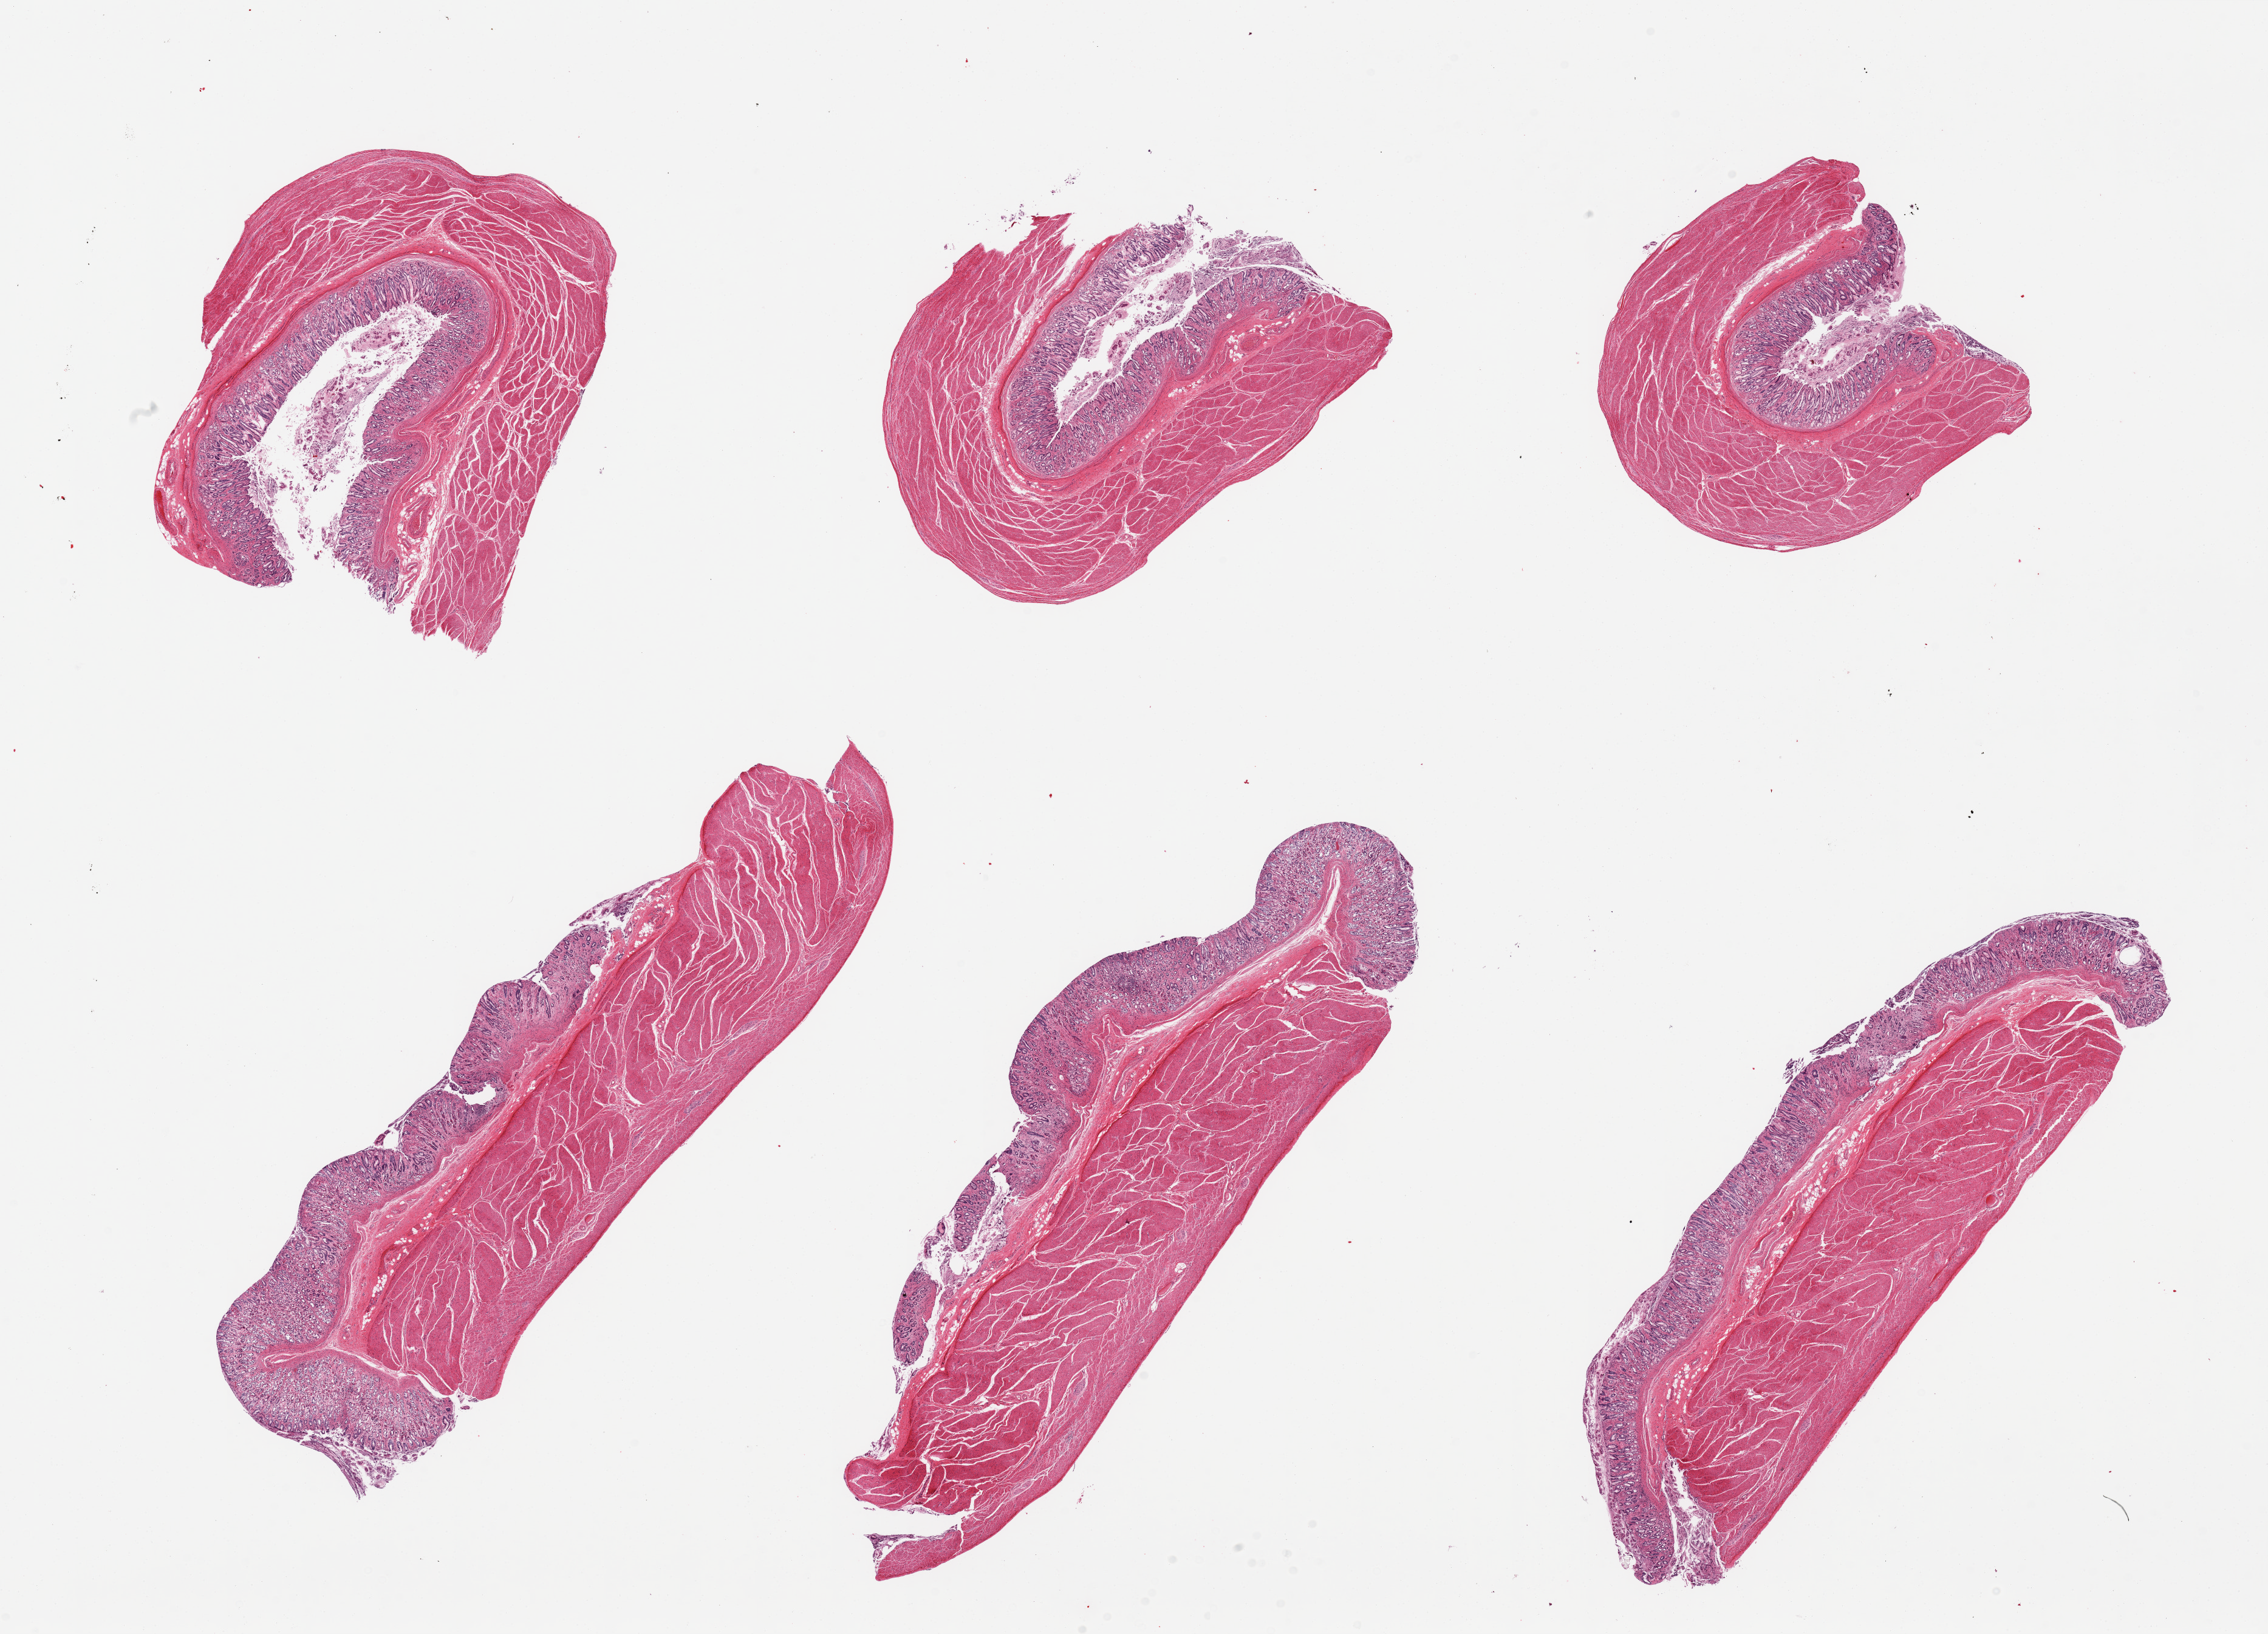
Whole-slide image, haematoxylin and eosin stain — whole scanned area (about 29.5 x 21.3 mm, from a 20x scan) shown as a low-resolution overview. PAXgene-fixed, paraffin-embedded tissue. Target tissue: stomach. Tissue donor sample. Donor: male.
Pathologist's review note for this sample: 6 pieces, mucosa and muscularis.